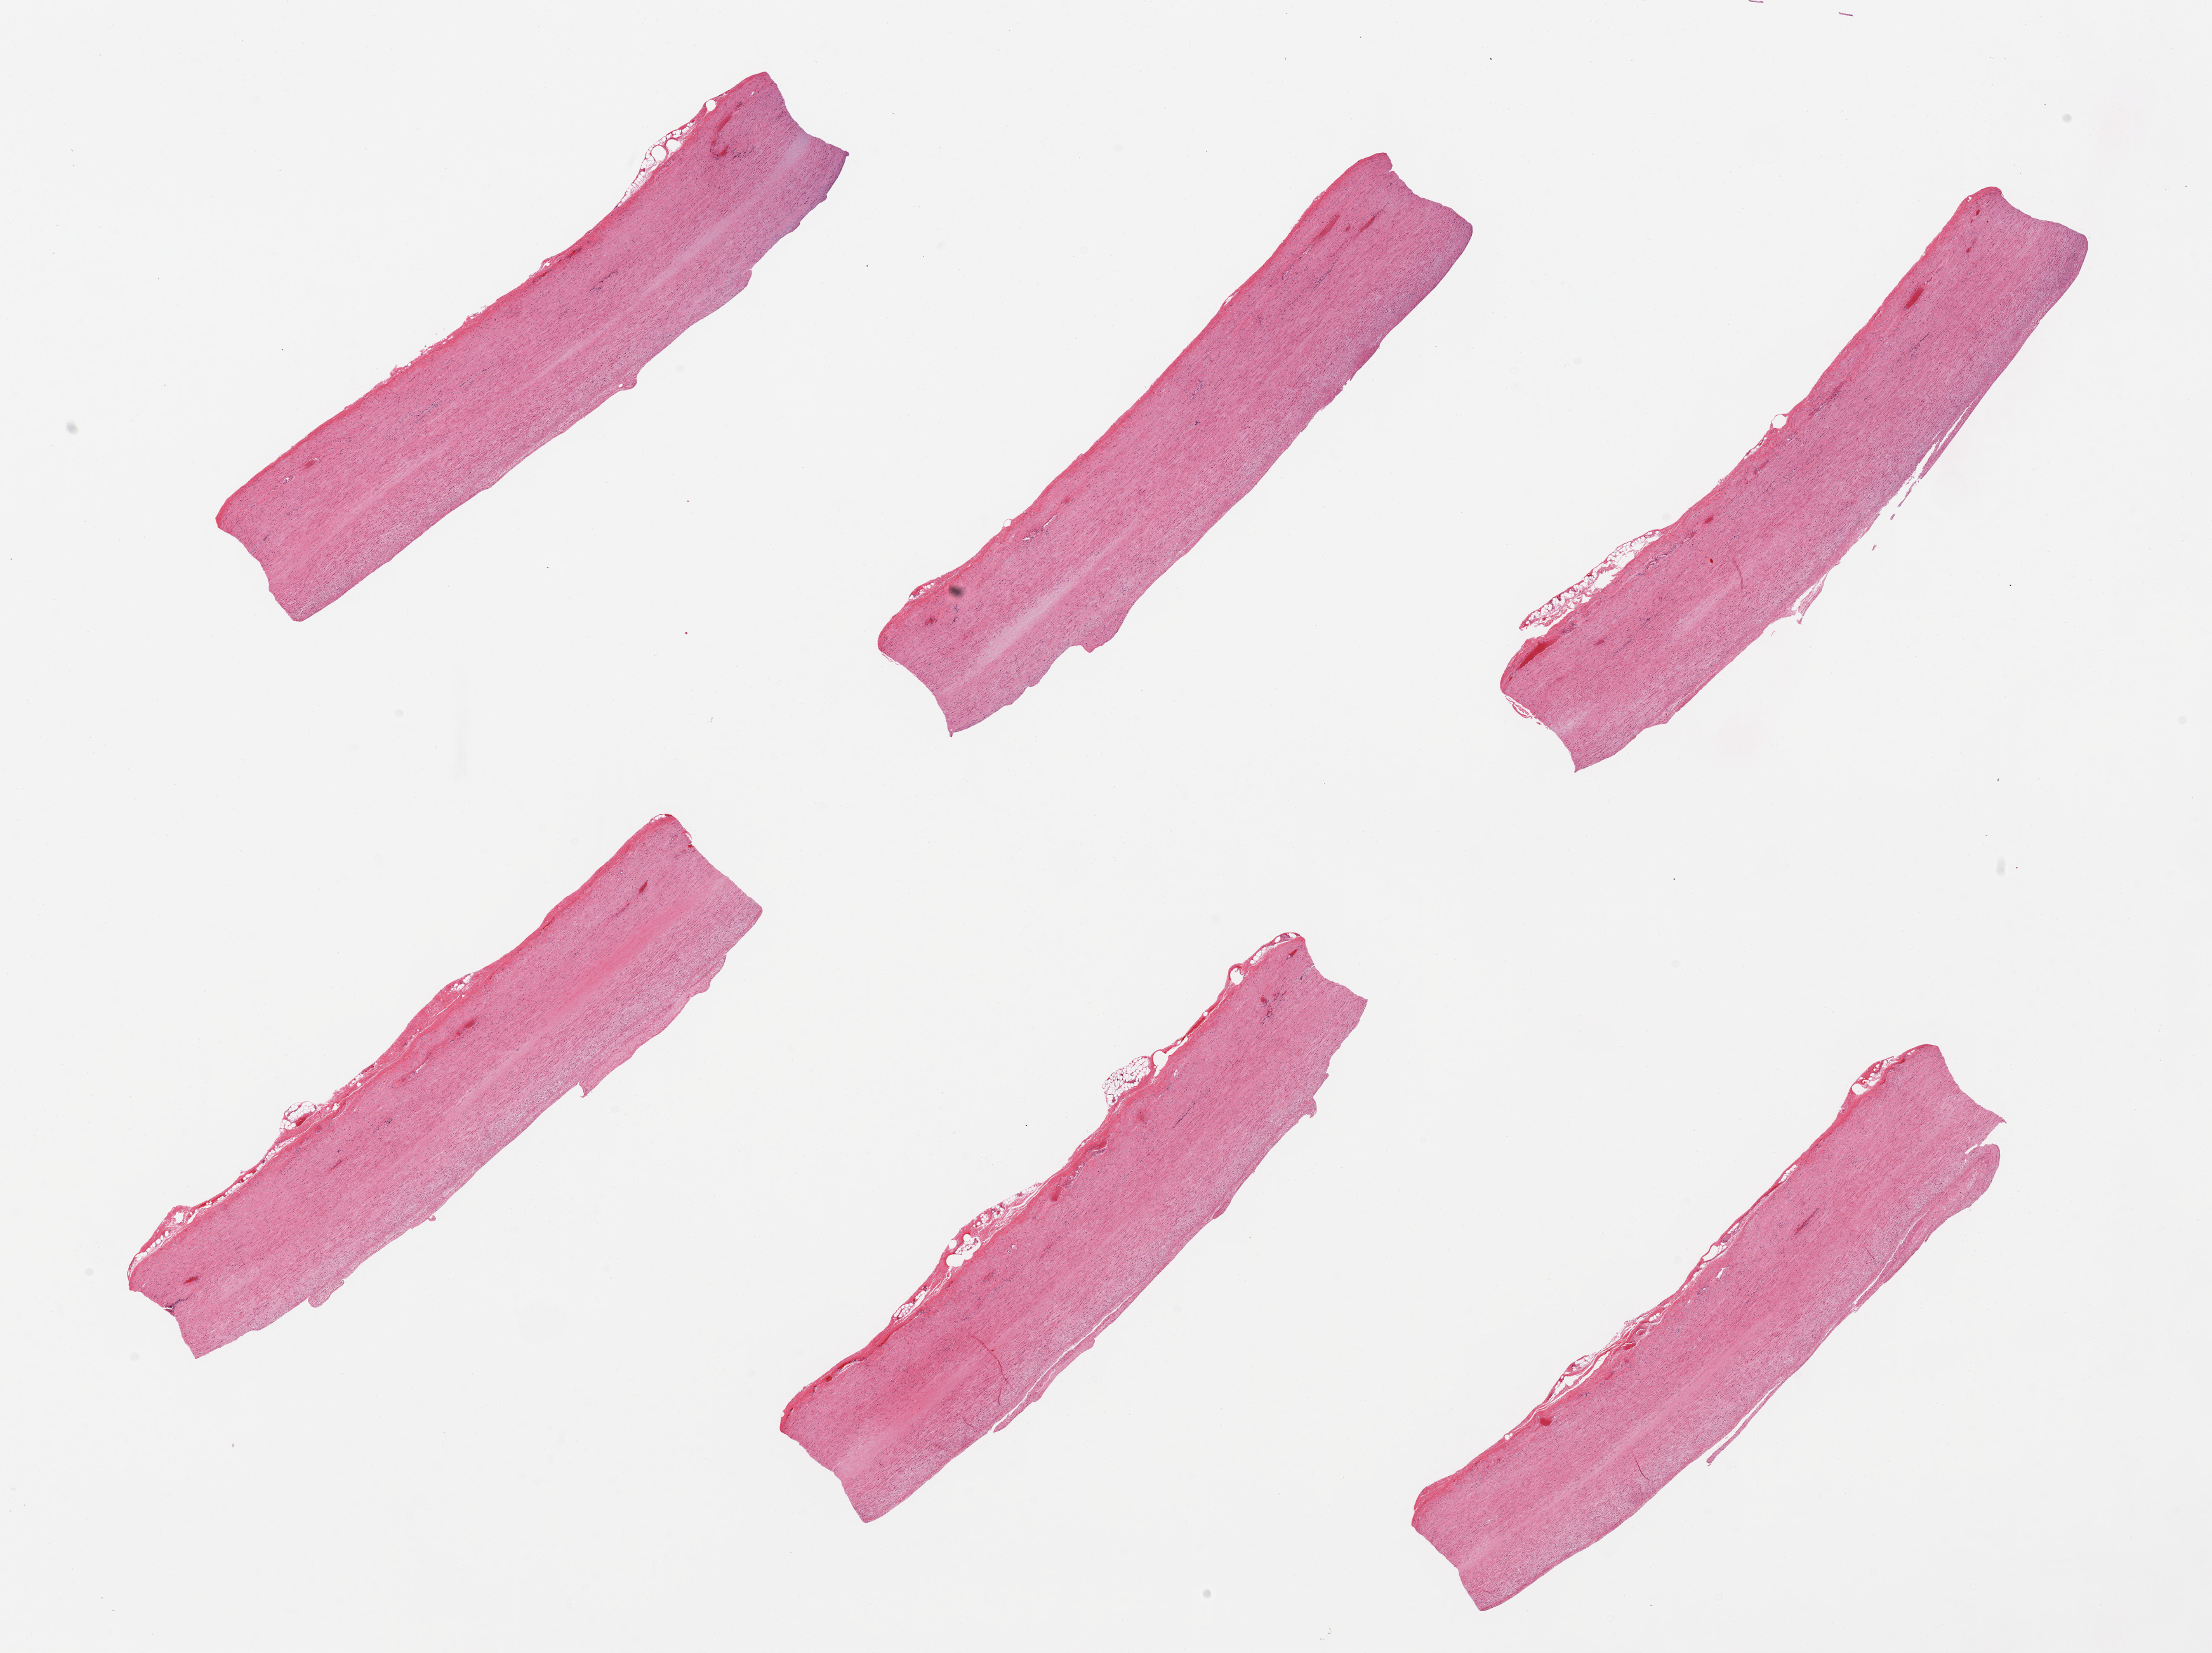
Haematoxylin and eosin whole-slide image — a low-resolution overview of the entire scanned area, about 27.6 x 20.6 mm (from a 20x scan); PAXgene-fixed, paraffin-embedded tissue; sampled site (target tissue): aorta; donor tissue sample.
• review note (as recorded): 6 pieces